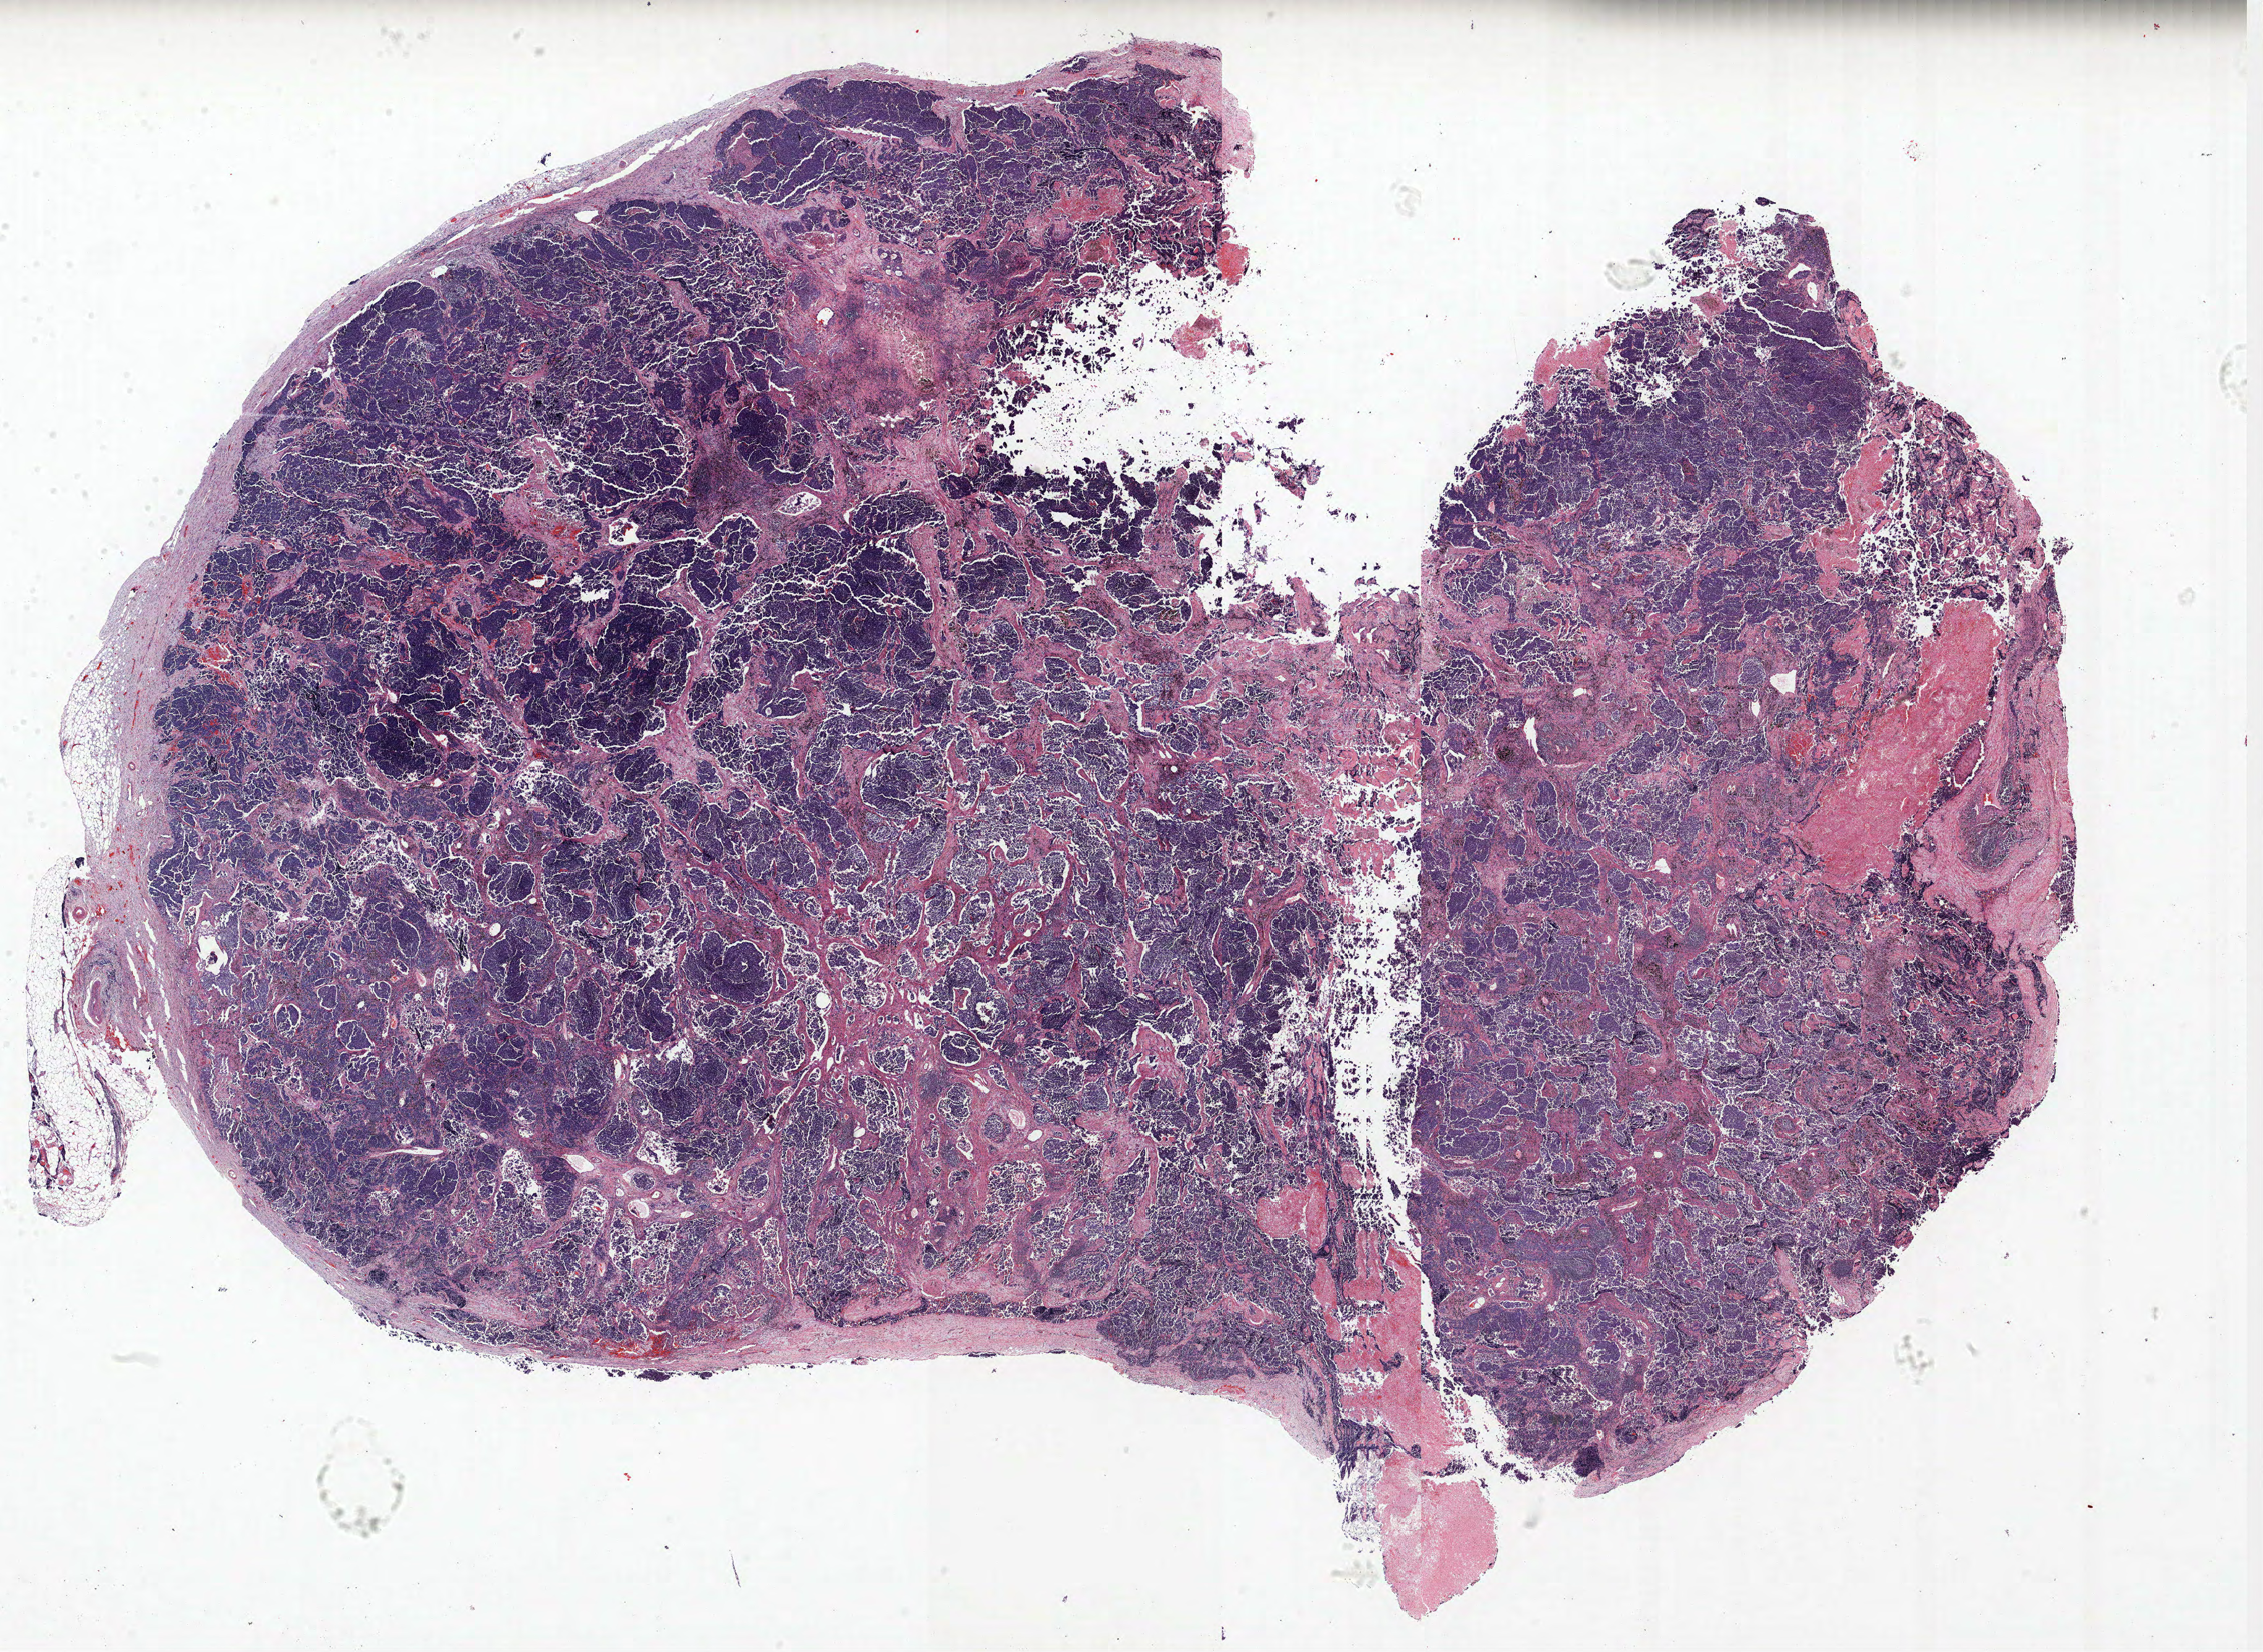
Hematoxylin and eosin (H&E) stained whole-slide image, whole scanned area (about 29.3 x 21.4 mm, acquisition: 40x scan) shown as a low-resolution overview, formalin-fixed paraffin-embedded (FFPE) section, lung. Male patient, aged 73 at enrolment.
Participant's lung-cancer diagnosis: Small cell carcinoma, NOS (ICD-O-3 8041/3).